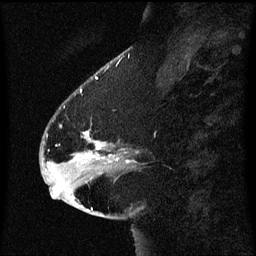
Breast MRI (dynamic contrast-enhanced), one sagittal slice; position 20 of 60 along the scan axis; dynamic contrast-enhanced series, image 2 of 3 at this slice position (ordered by acquisition); 1.5 T; TE 4.2 ms, TR 8.4 ms; 2 mm slice thickness; 256 × 256 image matrix, field of view 200 × 200 mm. Female patient, age 54 years. Case-level facts recorded for this patient, not image findings: setting: breast cancer imaged before/during neoadjuvant chemotherapy; receptor status: HR-positive, HER2-negative.
Outlined on this slice (semi-automatically segmented with operator editing):
- analysis volume of interest (the breast-tissue region the enhancement analysis was run in; not a lesion): bounding box <46,102,123,171> (left, top, right, bottom; pixels)
- tumour enhancement mask (voxels above the 70 % enhancement threshold inside the analysis volume of interest): <78,132,118,161>